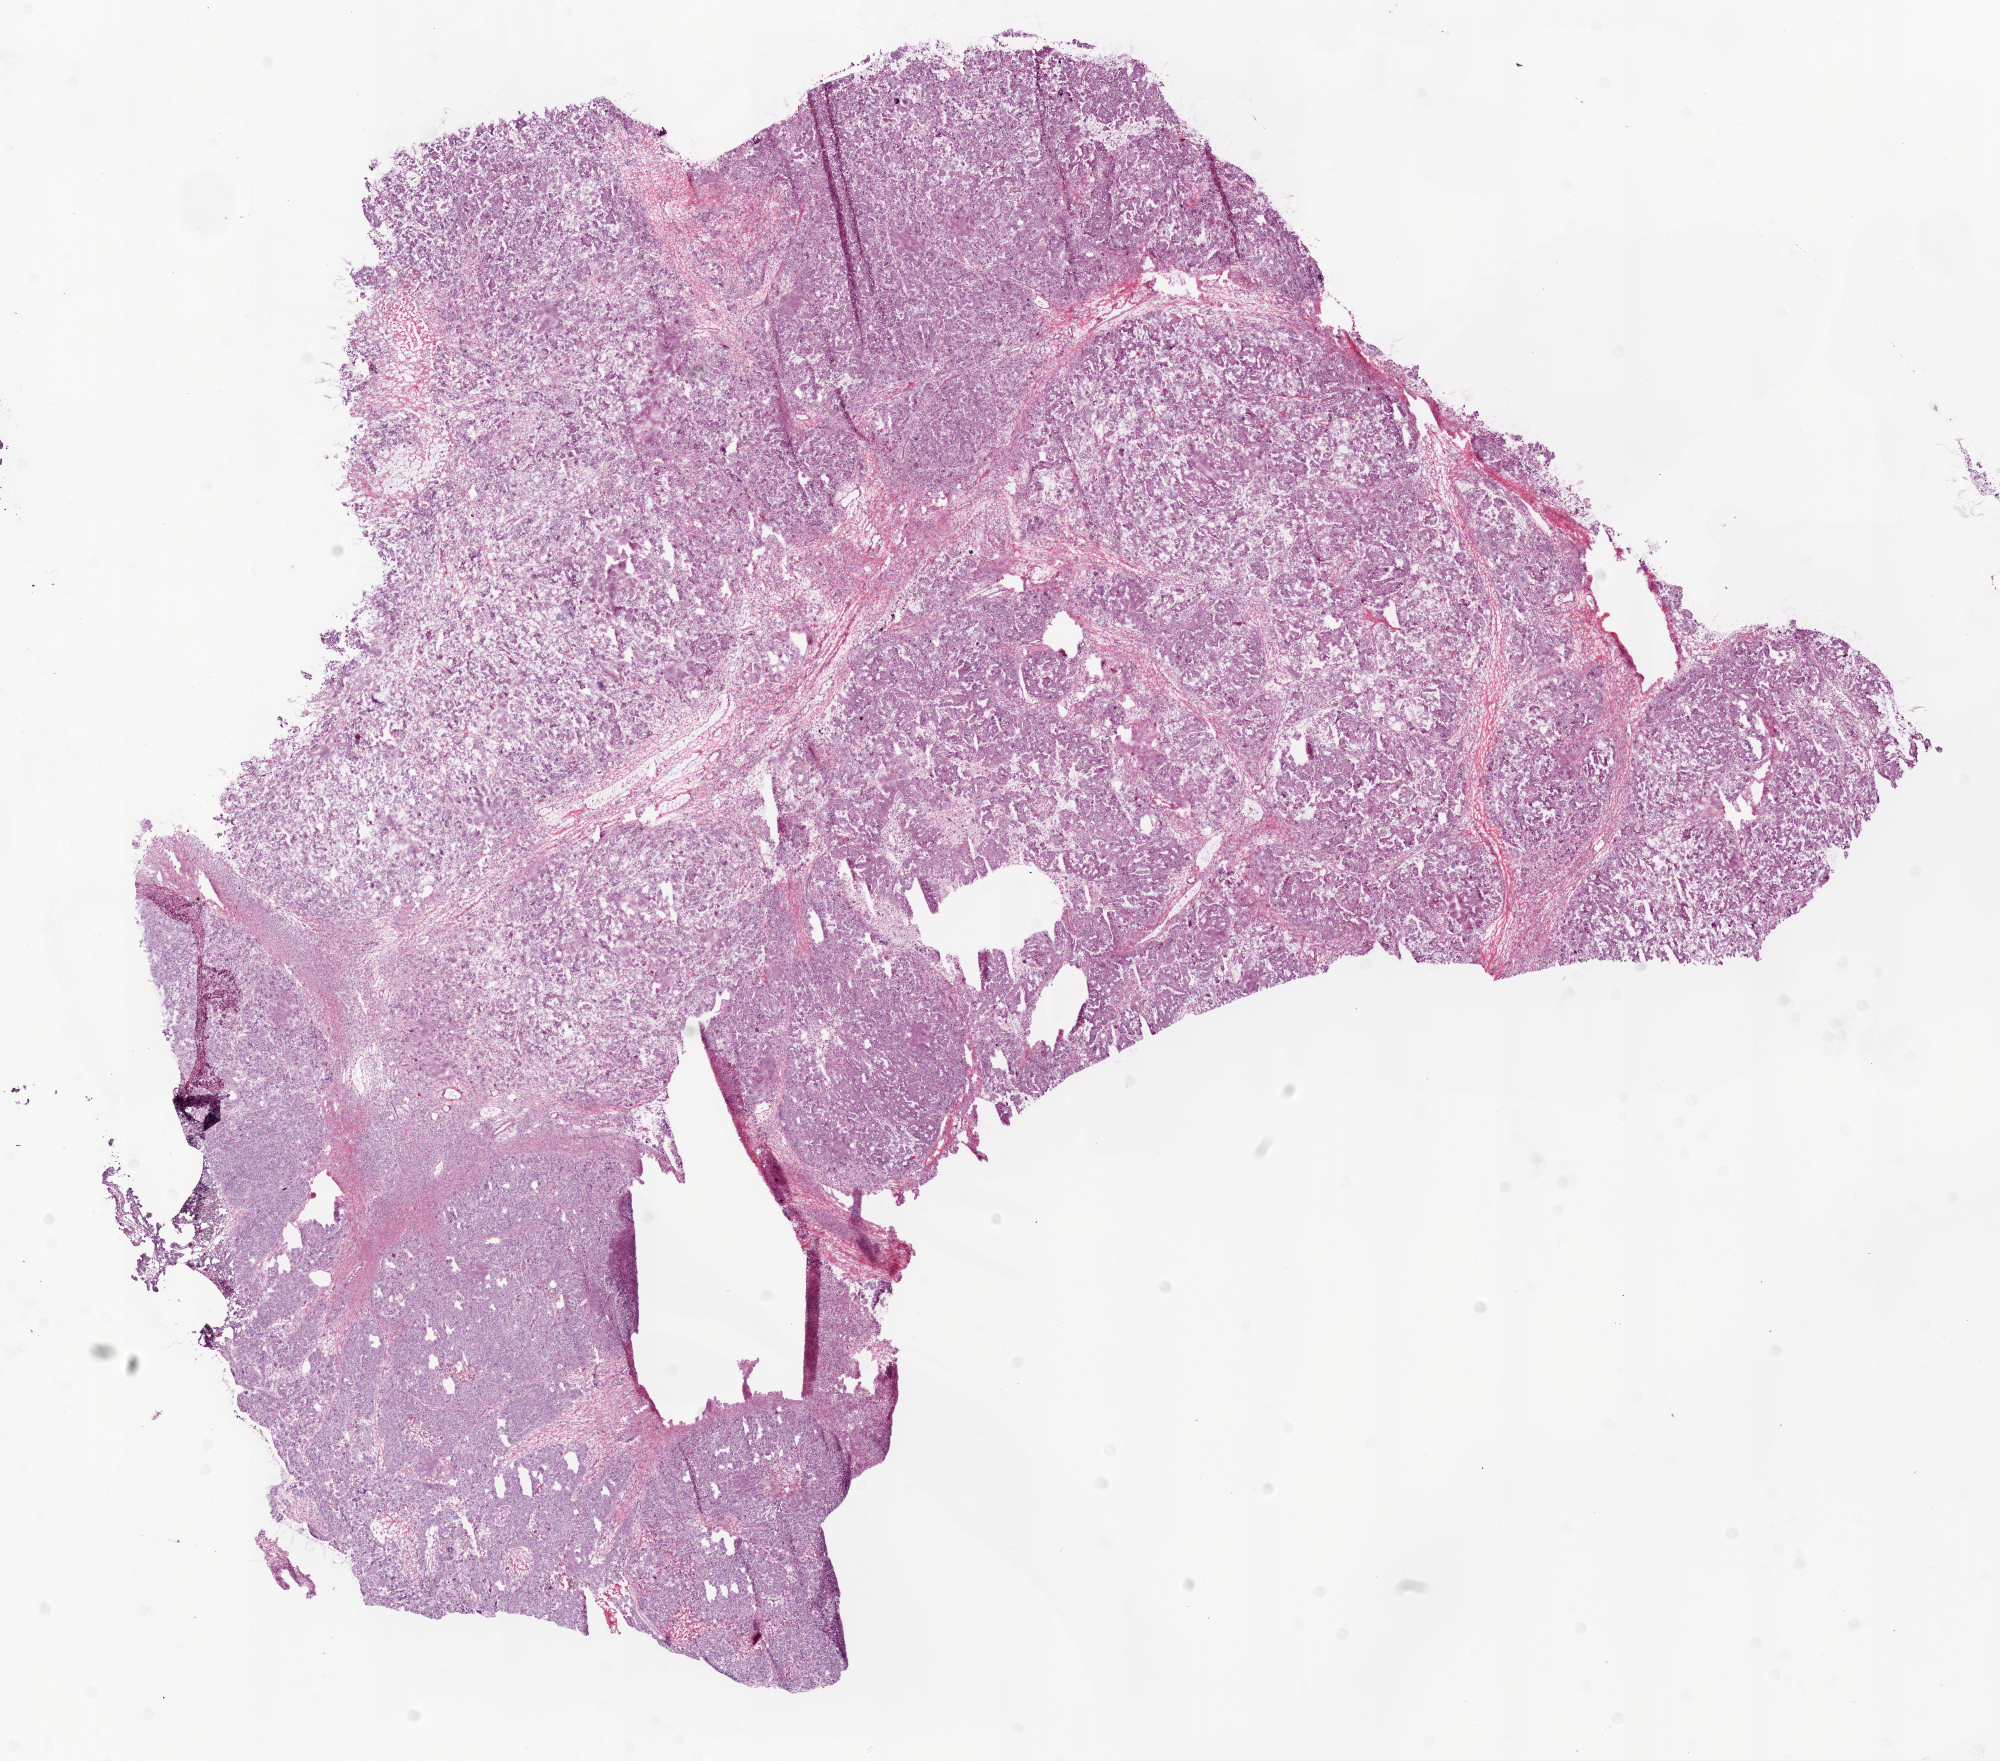
H&E whole-slide image, a low-resolution overview of the entire scanned area, about 16.0 x 14.1 mm (slide scanned at 20x). Frozen section from the top of the tissue portion. Sample: primary tumour, ovary. Female, age 65 years at initial diagnosis.
Diagnosis: Serous cystadenocarcinoma, NOS.